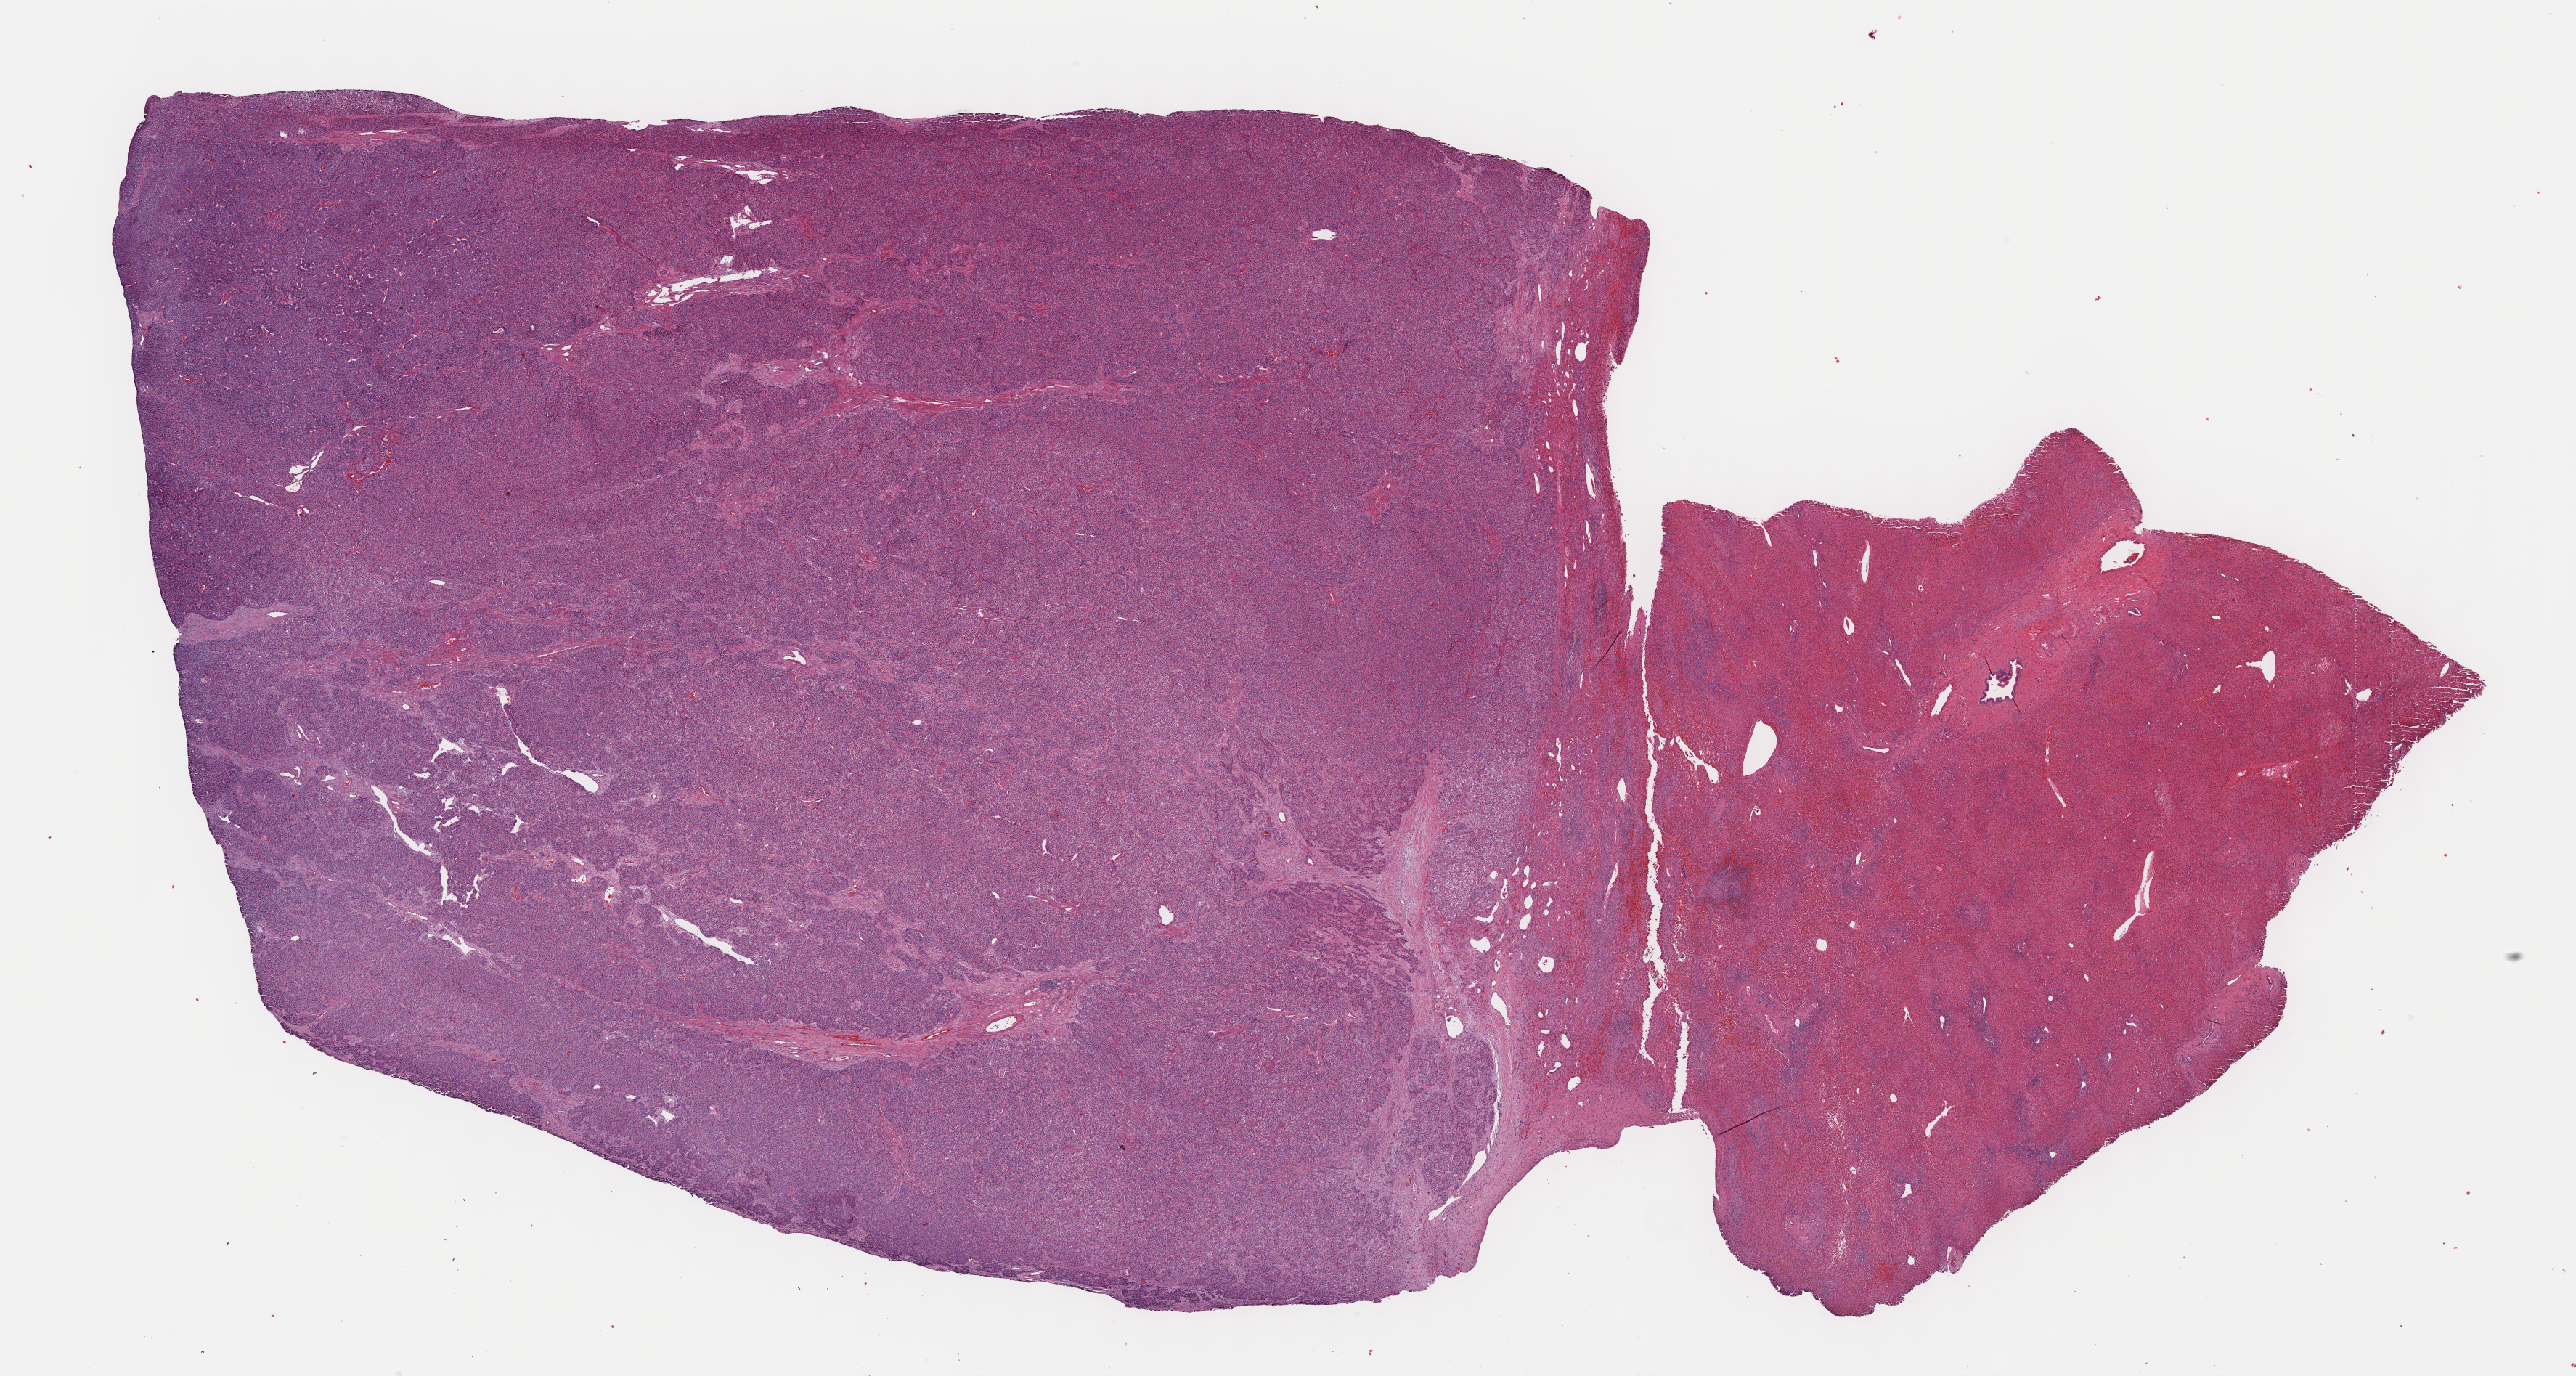
Hematoxylin and eosin (H&E) stained whole-slide image — shown as a low-resolution overview of the whole scanned area (about 28.7 x 15.3 mm, from a 40x scan), FFPE section, primary tumour sample from the liver. Female patient; age at initial diagnosis 56 years. Histologic grade: G3 (poorly differentiated).
Diagnosis: Hepatocellular carcinoma, NOS. AJCC pathologic stage: I (6th edition).